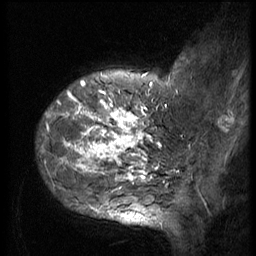
Breast MRI (dynamic contrast-enhanced), one sagittal slice. Position 12 of 56 along the scan axis. 3 images stored at this slice position (order not interpretable as contrast timing). 1.5 T. TE 4.2 ms, TR 9 ms. 2.5 mm slice thickness. 256 × 256 image matrix. Patient: female, 49 years. From the clinical record (not read from this slice): setting: breast cancer imaged before/during neoadjuvant chemotherapy; receptor status: HER2-positive.
Structures marked on this image (semi-automatically segmented with operator editing):
- analysis volume of interest (the breast-tissue region the enhancement analysis was run in; not a lesion): box from (x=37, y=85) to (x=162, y=207) px
- tumour enhancement mask (voxels above the 140 % enhancement threshold inside the analysis volume of interest): (x=43, y=85)–(x=158, y=207)